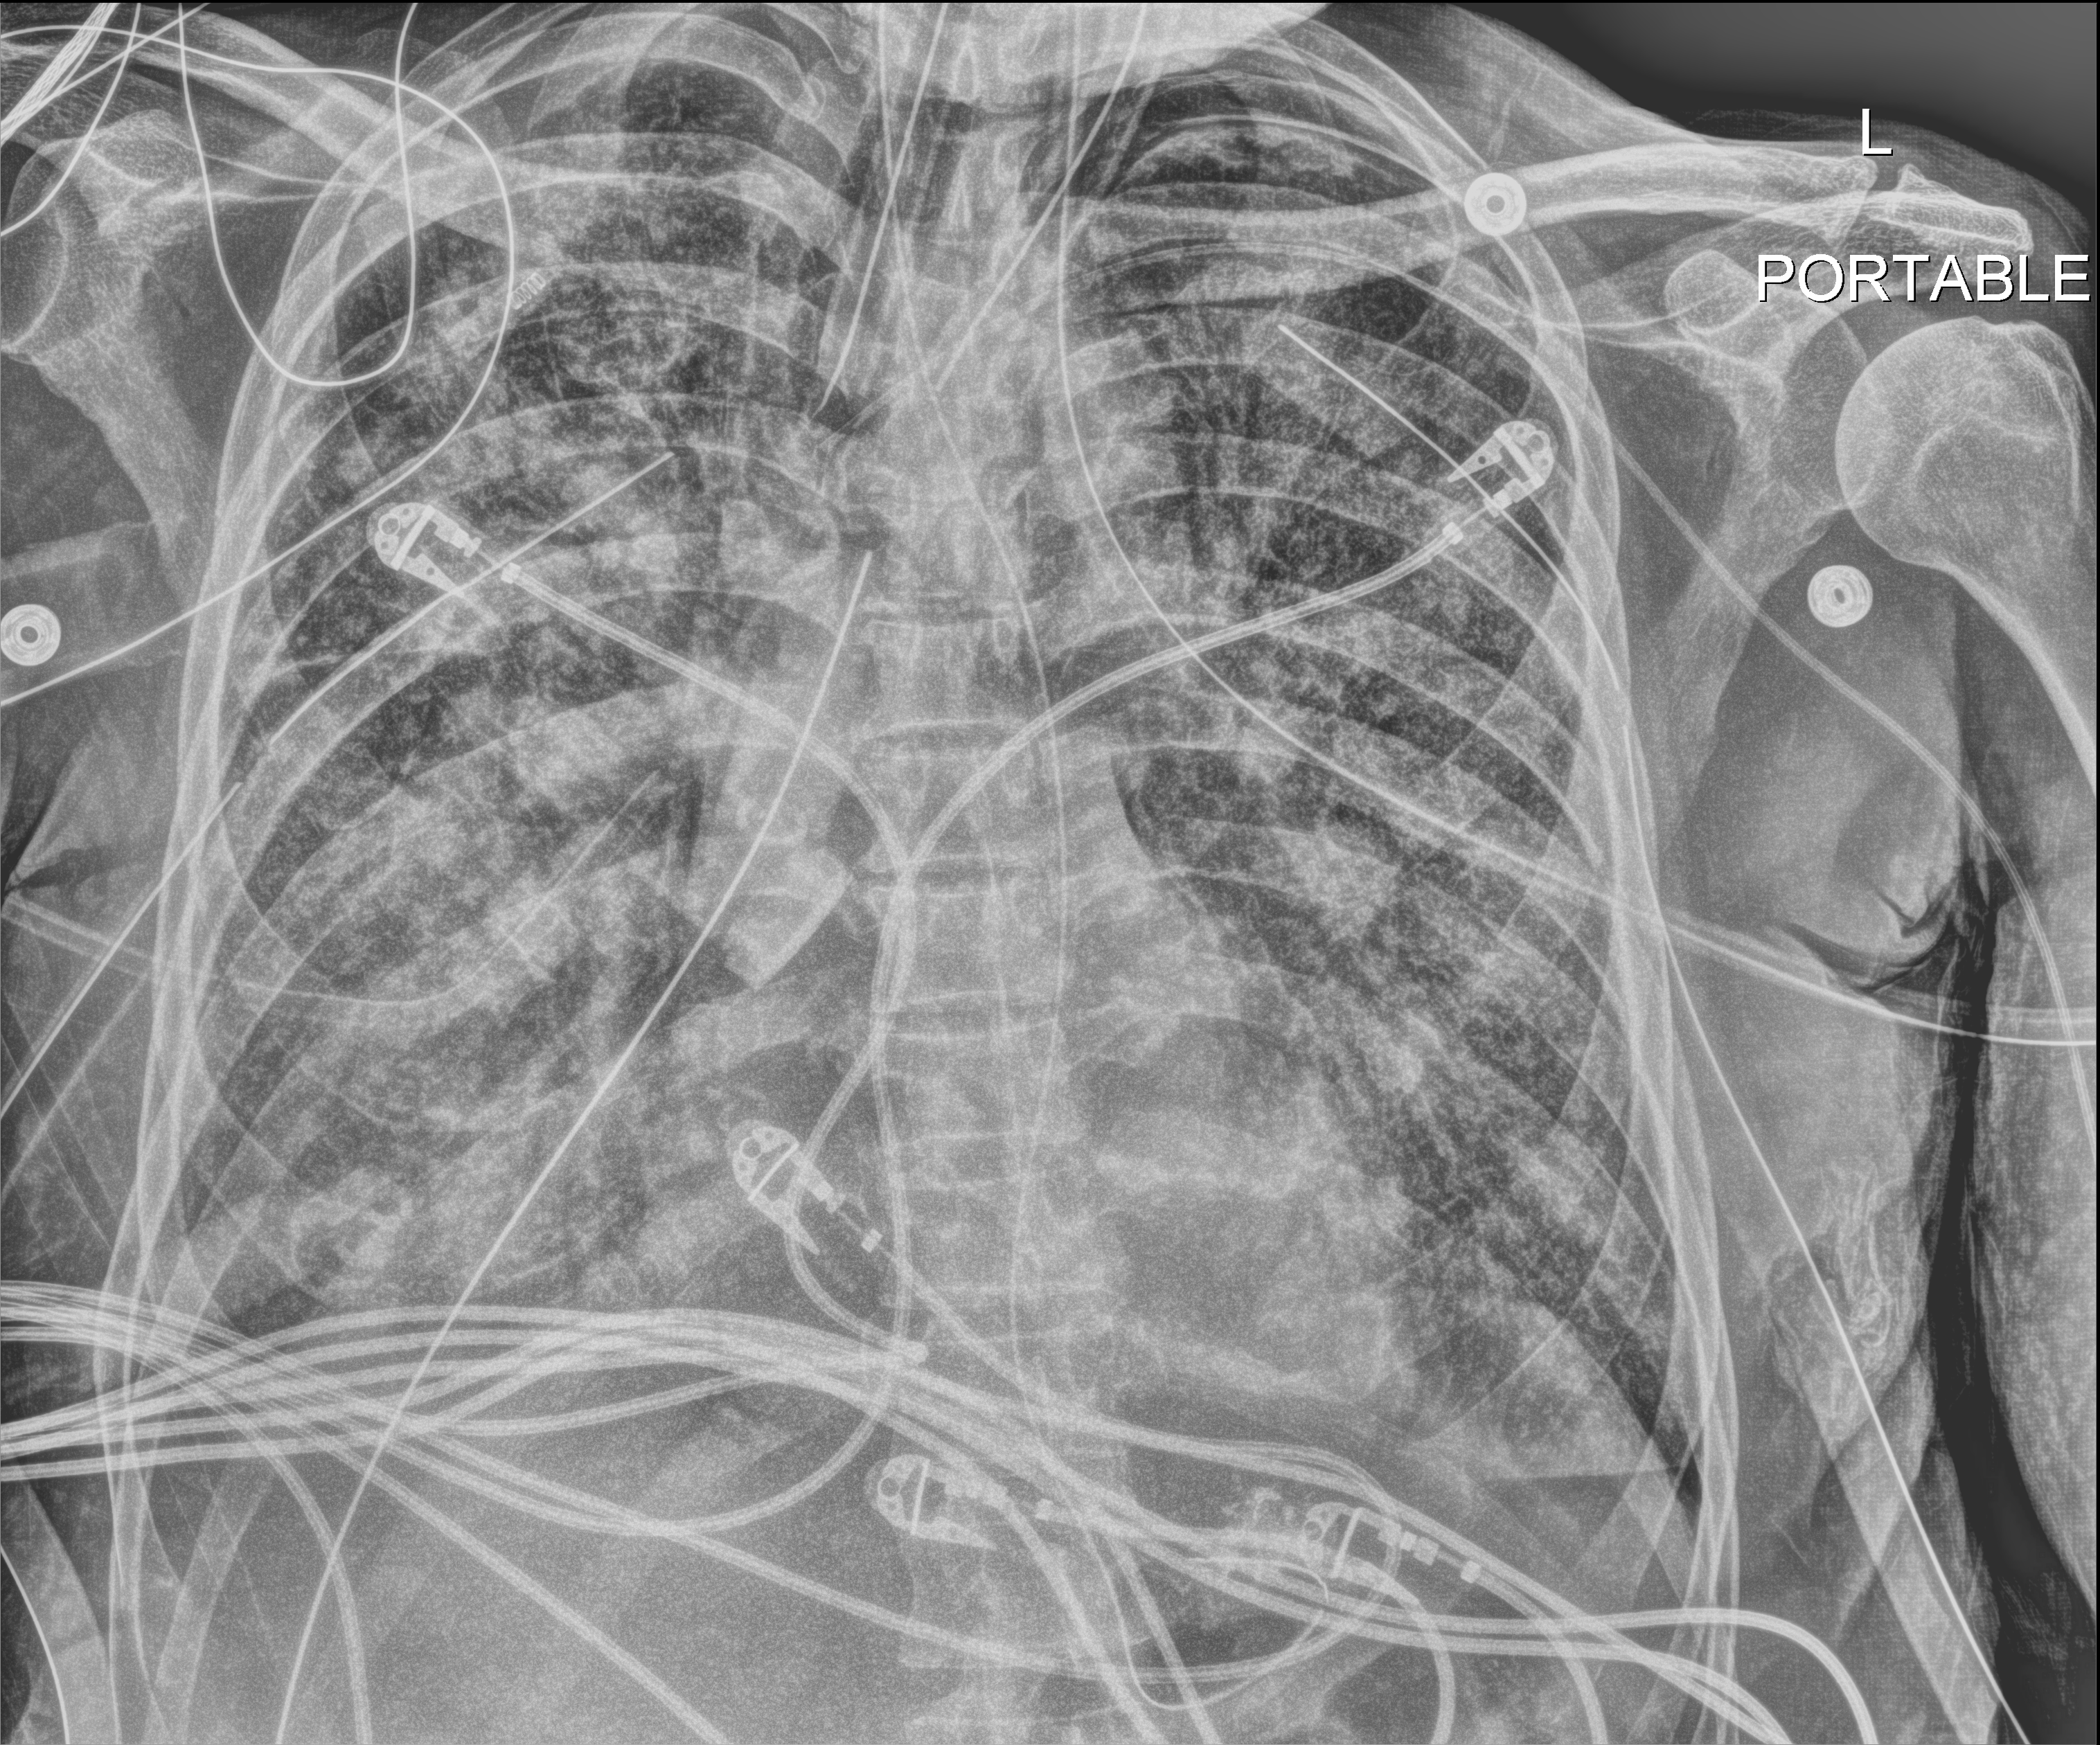
Bedside chest radiograph (digital radiography); anteroposterior (AP) projection. Male patient hospitalised with COVID-19, age 60–74 years.
Admission-level facts for this patient (not findings on this image; timing relative to this image not recorded):
- smoking status (admission record): former
- mechanically ventilated during this hospital stay: yes
- hypertension (admission record): no